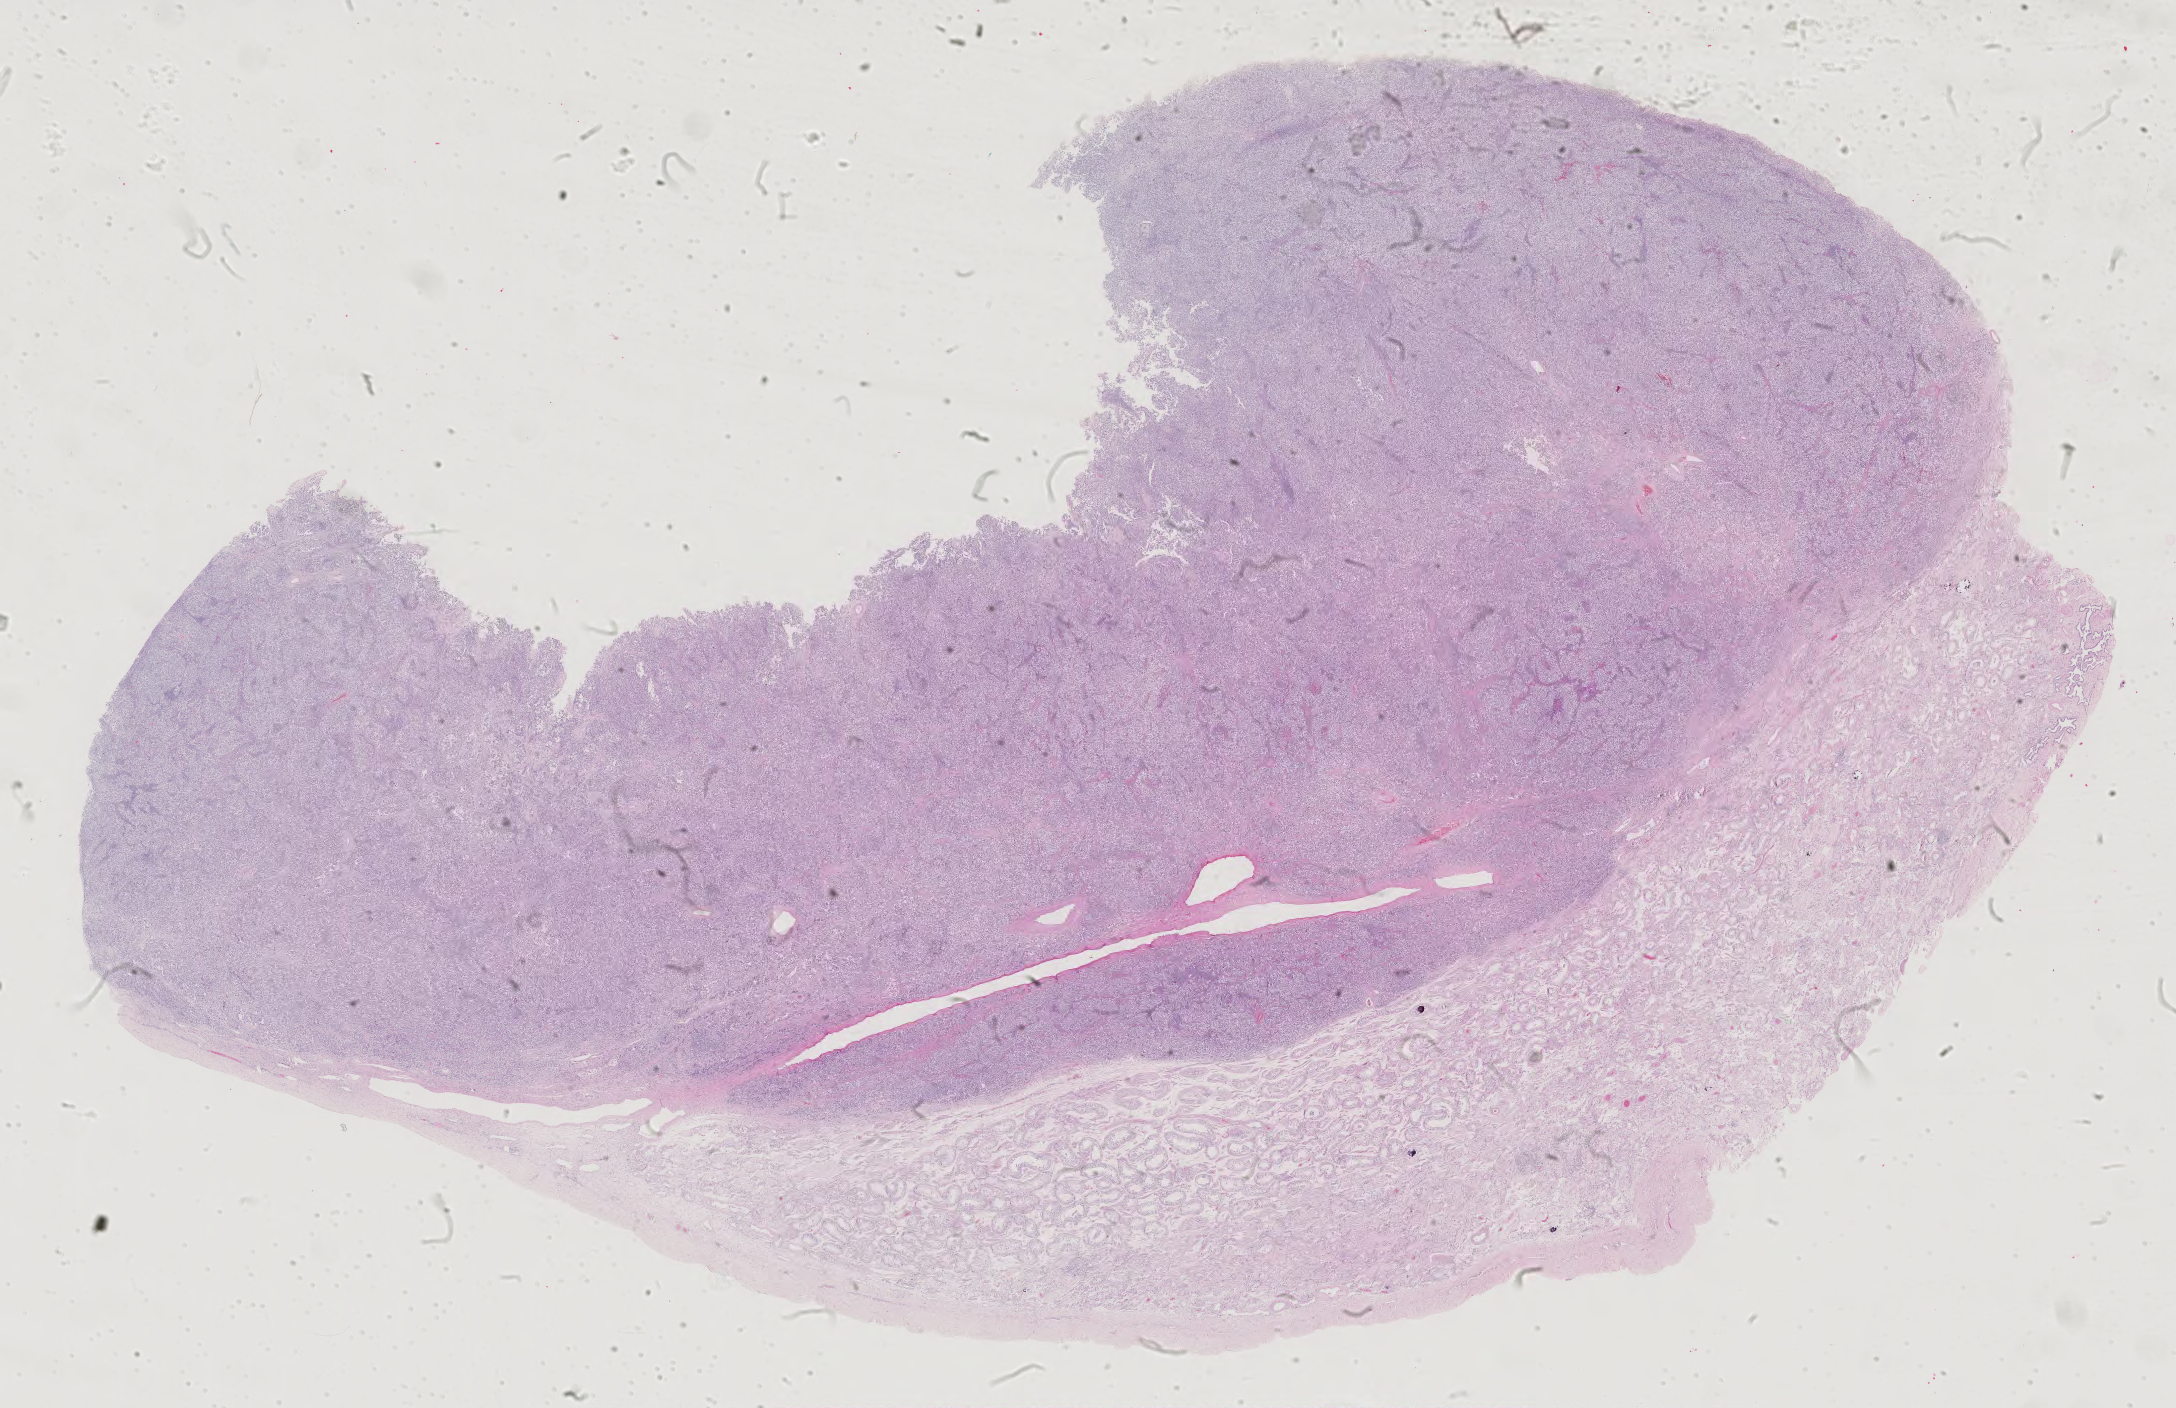
Whole-slide histology image, Hematoxylin and eosin (H&E) stained, shown as a low-resolution overview of the whole scanned area (about 31.7 x 20.5 mm, slide scanned at 40x); formalin-fixed paraffin-embedded (FFPE) diagnostic section; sample: primary tumour, testis. Male, age 33 years at initial diagnosis.
* AJCC pathologic stage: IA (6th edition)
* pathologic diagnosis: Seminoma, NOS